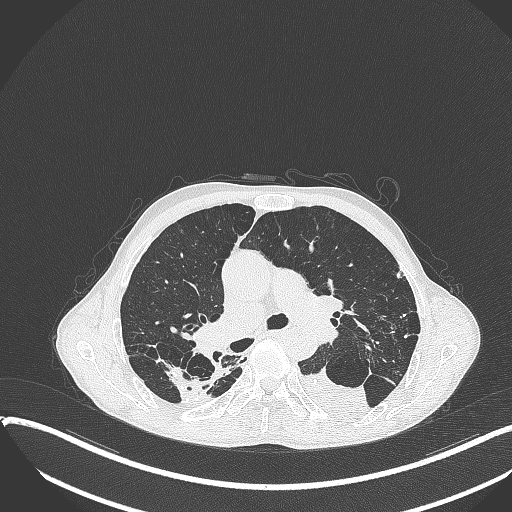
Chest CT, one axial slice; reconstruction kernel B70f; lung window (W 1500 / L -600 HU); 1 mm slice thickness; 512 × 512 image matrix, field of view 400 × 400 mm. Patient: male, 57 years. Case-level facts recorded for this patient, not image findings: clinical TNM (as recorded): T4 N0 M0.
Outlined on this slice (rectangle marked by the reading radiologist):
- lung tumour (recorded histology: squamous cell carcinoma): bounding box [x1, y1, x2, y2] px = [299, 365, 374, 418]